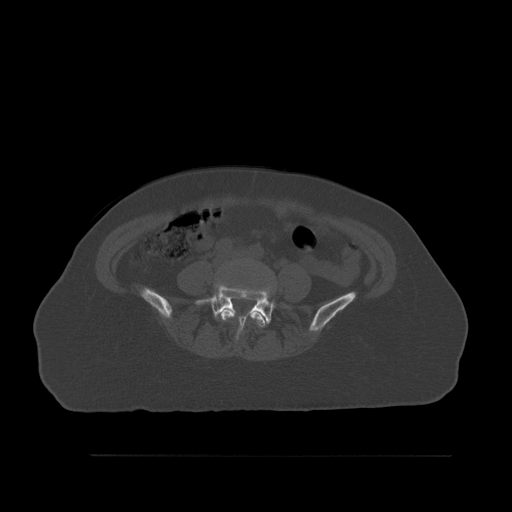
CT including the spine, one axial slice; bone window (W 1800 / L 400 HU); 1.5 mm slice thickness; 512 × 512 image matrix. Patient: female, 73 years. Case-level facts recorded for this patient, not image findings: primary cancer: breast.
Structures marked on this image (semi-automatically segmented with operator editing):
- L4 vertebra: box from (x=221, y=303) to (x=267, y=337) px
- L5 vertebra: (x=196, y=284)–(x=282, y=338)